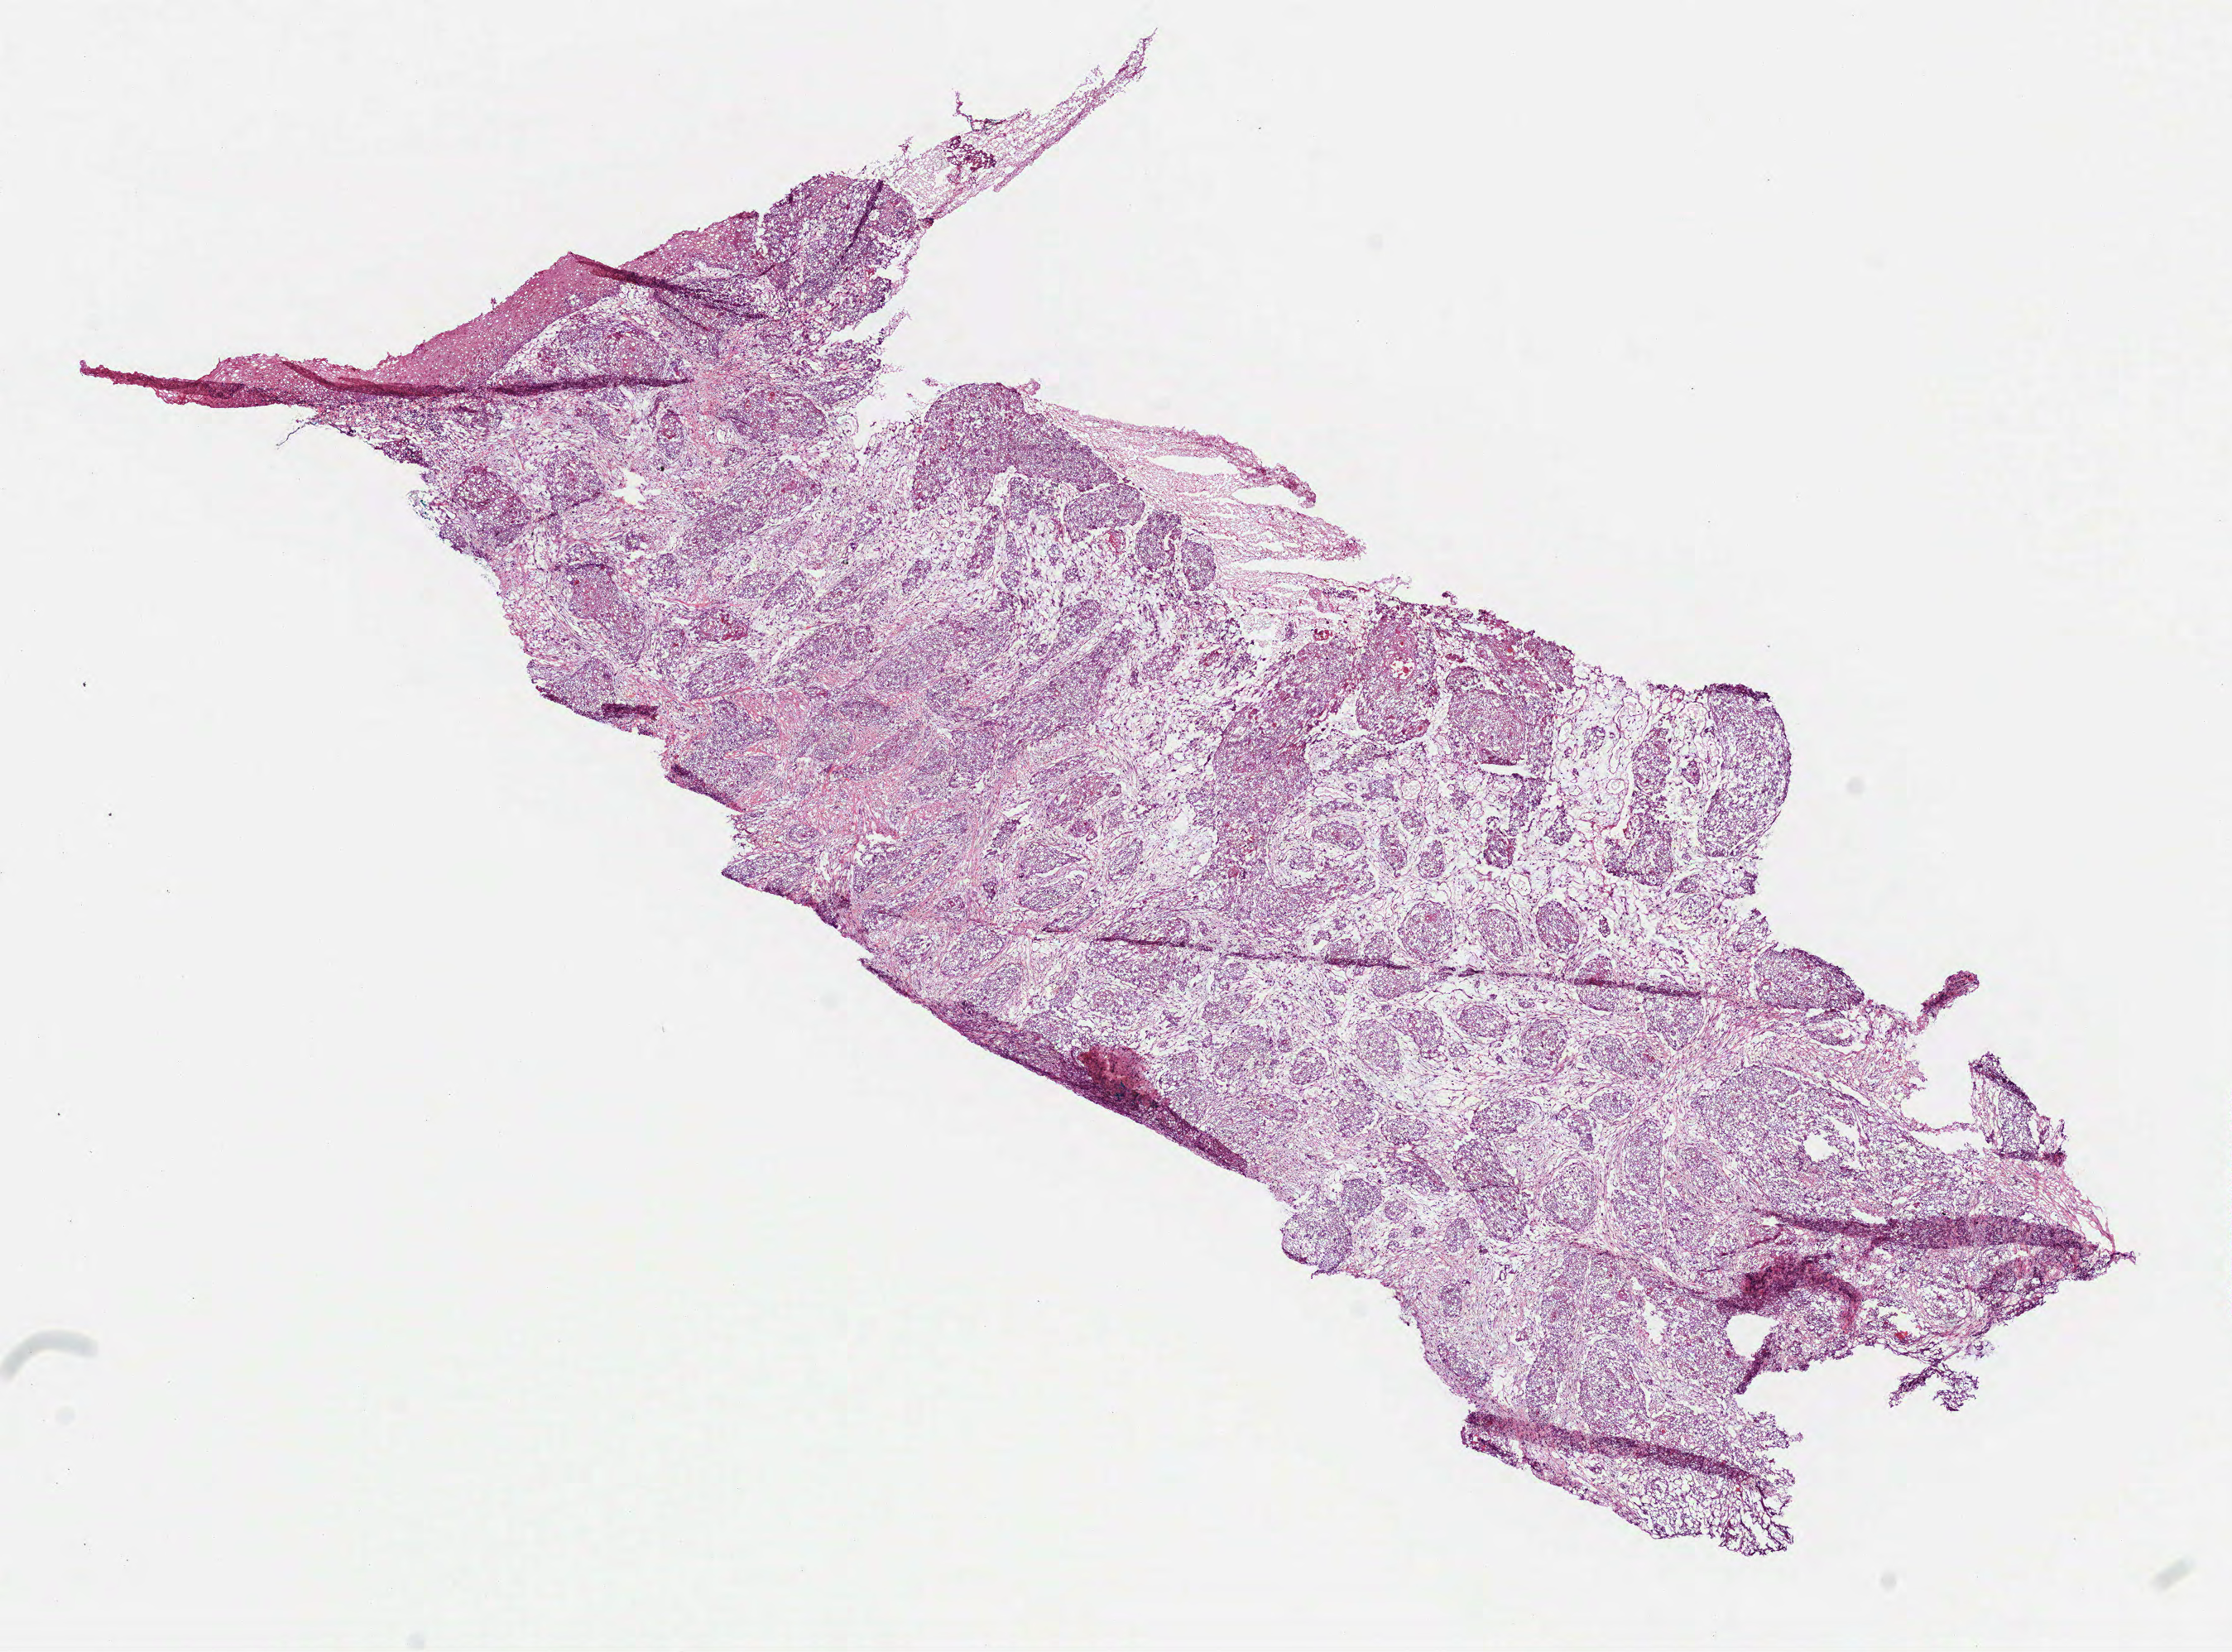
Whole-slide histology image, H&E — shown as a low-resolution overview of the whole scanned area (about 10.9 x 8.1 mm), frozen section, head and neck, primary tumour sample. Male patient; age at initial diagnosis 61 years. Histologic grade: G1 (well differentiated). Composition of this section per pathologist review: tumour cells 100%, tumour nuclei 70%, normal cells 0%, stromal cells 0%, necrosis 0%. Inflammatory infiltration, as recorded: lymphocyte infiltration 10%, monocyte infiltration 0%, neutrophil infiltration 3%.
* lymph nodes positive (case pathology): 1 of 17 examined
* AJCC pathologic stage: III (7th edition)
* pathologic diagnosis: Squamous cell carcinoma, NOS